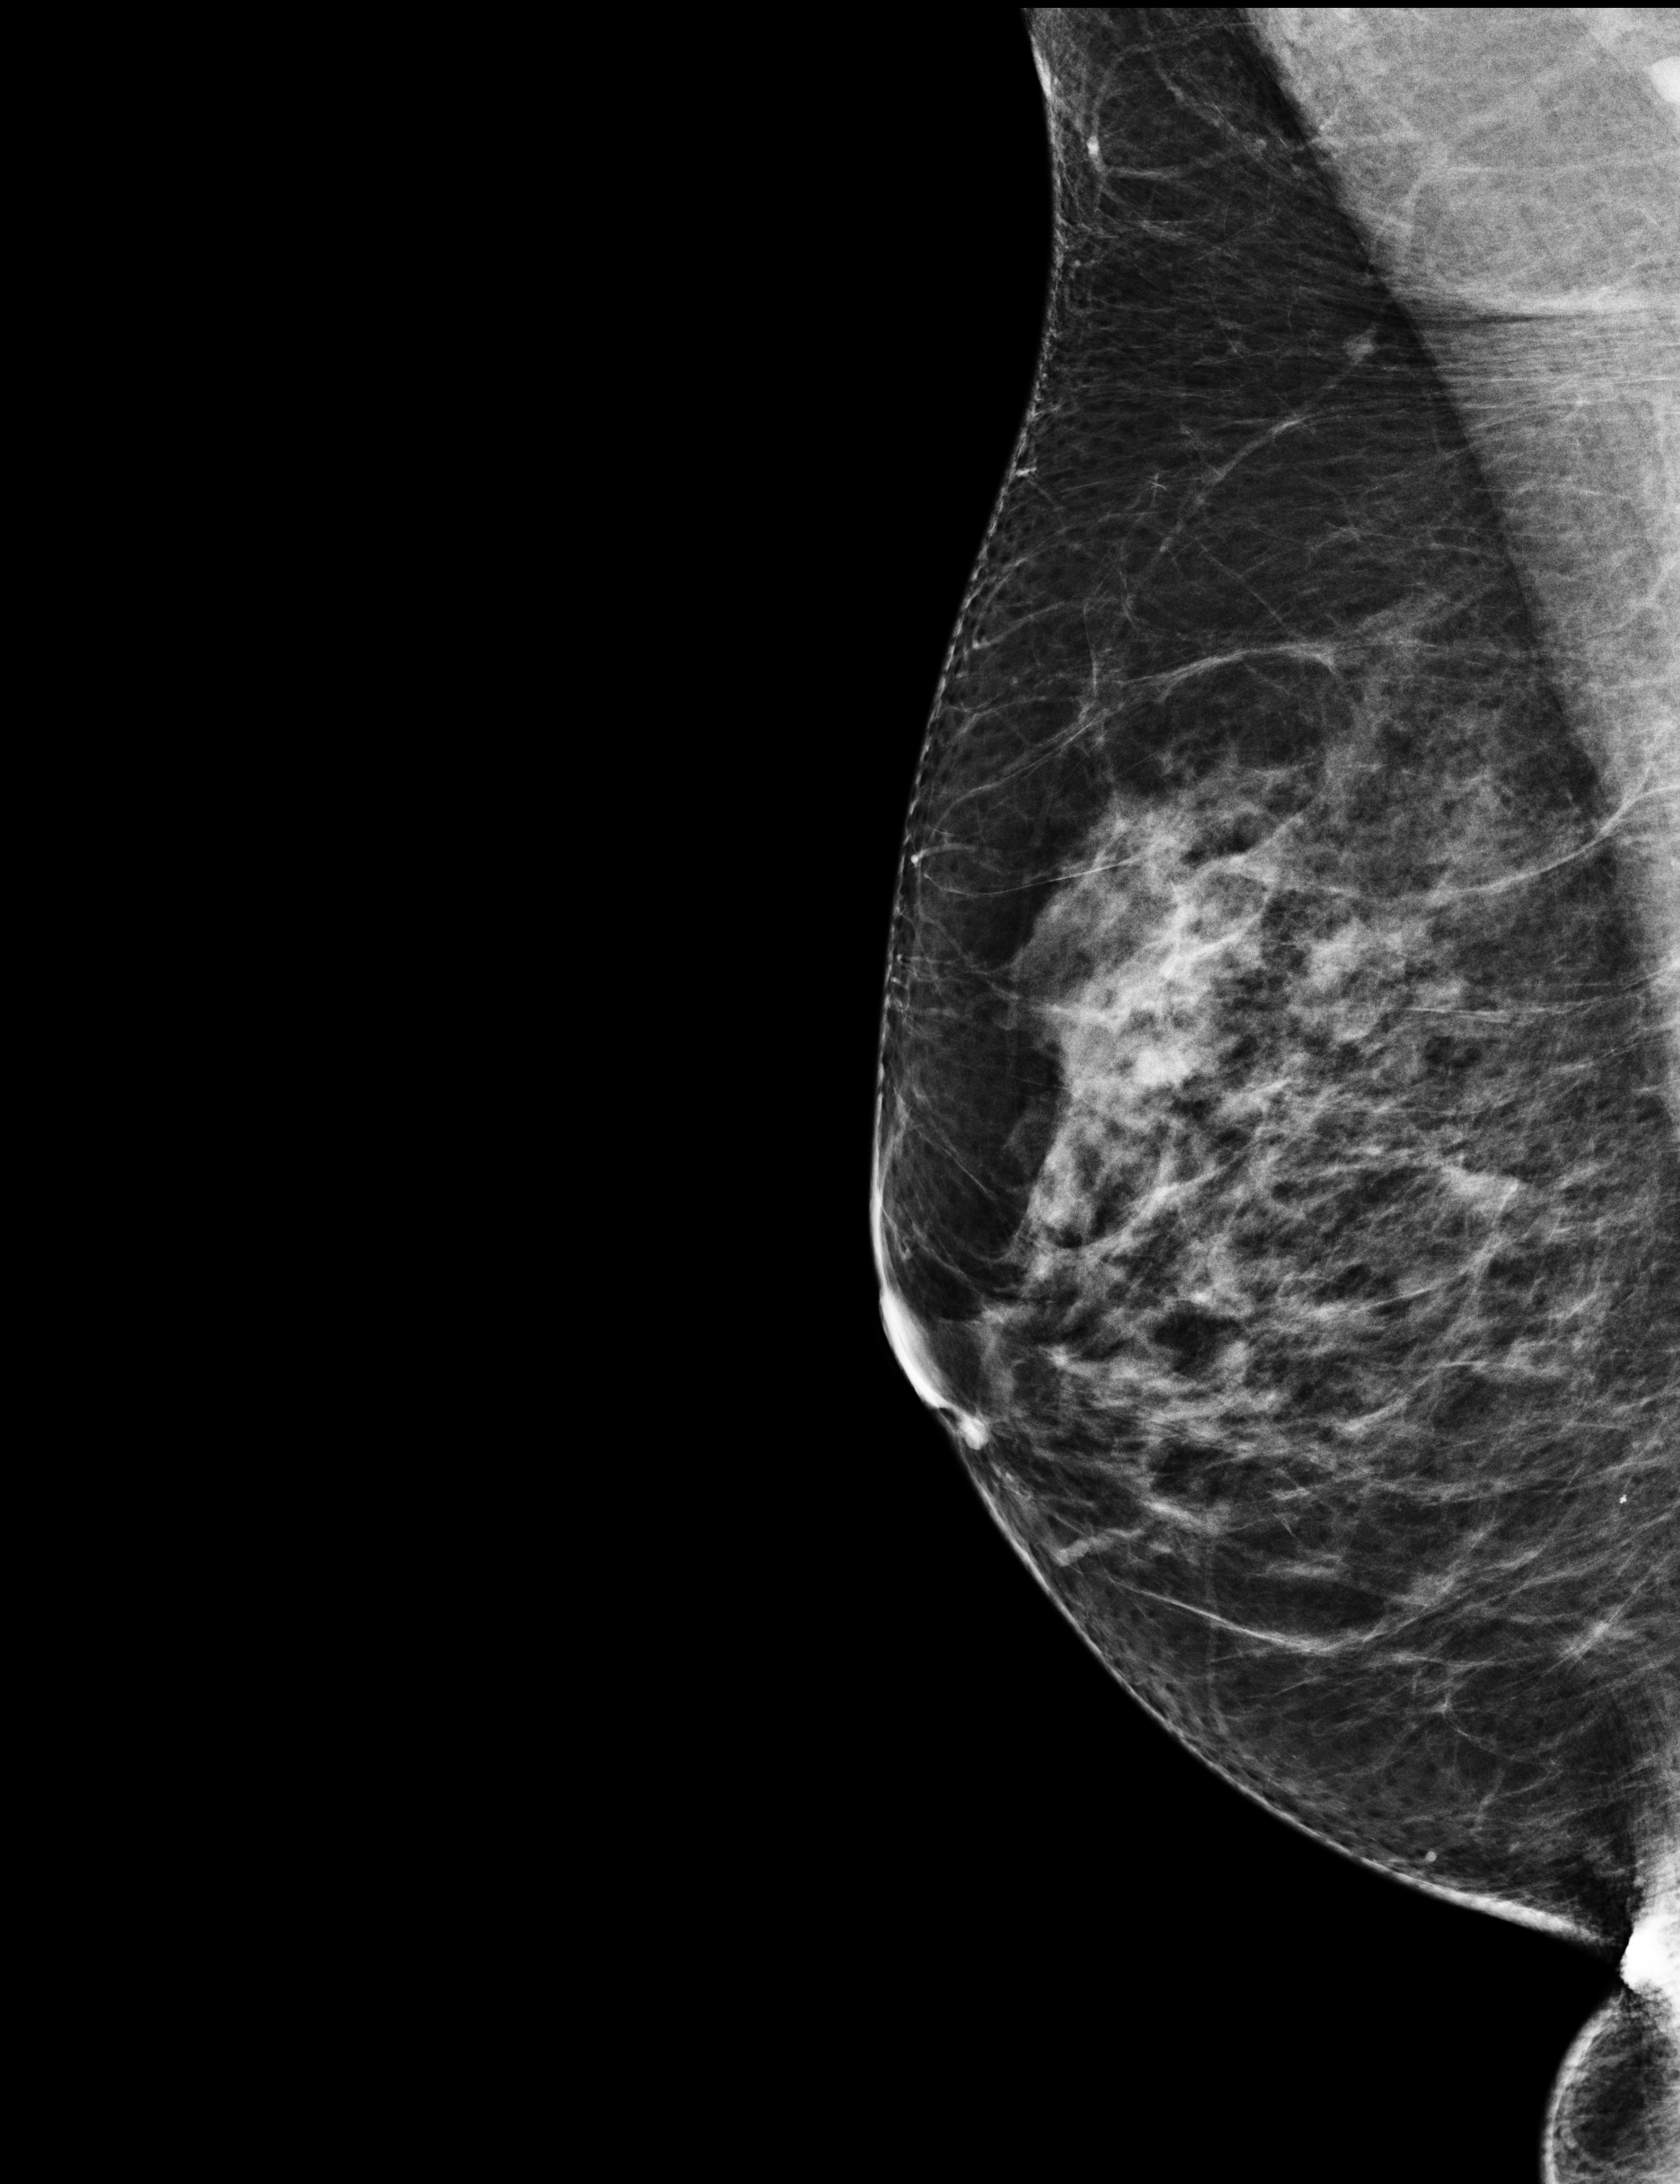
Annual screening mammography examination; compressed breast thickness 57 mm. Patient: female, 55 years.
Image type: full-field digital mammogram. Breast: right. Projection: MLO view.